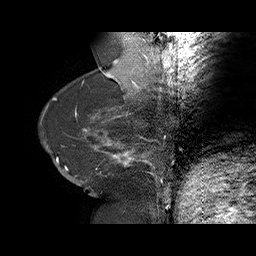
Breast MRI (dynamic contrast-enhanced), one sagittal slice. Slice 22 of 75 in the series (ordered by position). Dynamic contrast-enhanced series, time point 2 of 6 at this slice position (early post-contrast). 1.5 T. TE 4.5 ms, TR 32.4 ms. 3 mm slice thickness. 256 × 256 image matrix, field of view 180 × 180 mm. Female patient. Case-level facts recorded for this patient, not image findings: setting: breast cancer imaged before/during neoadjuvant chemotherapy; receptor status: HR-positive, HER2-negative.
Structures marked on this image (semi-automatic segmentation, software-assisted and operator-edited):
- analysis volume of interest (the breast-tissue region the enhancement analysis was run in; not a lesion): bounding box [x1, y1, x2, y2] px = [58, 134, 166, 191]
- tumour enhancement mask (voxels above the 100 % enhancement threshold inside the analysis volume of interest): [65, 139, 159, 186]